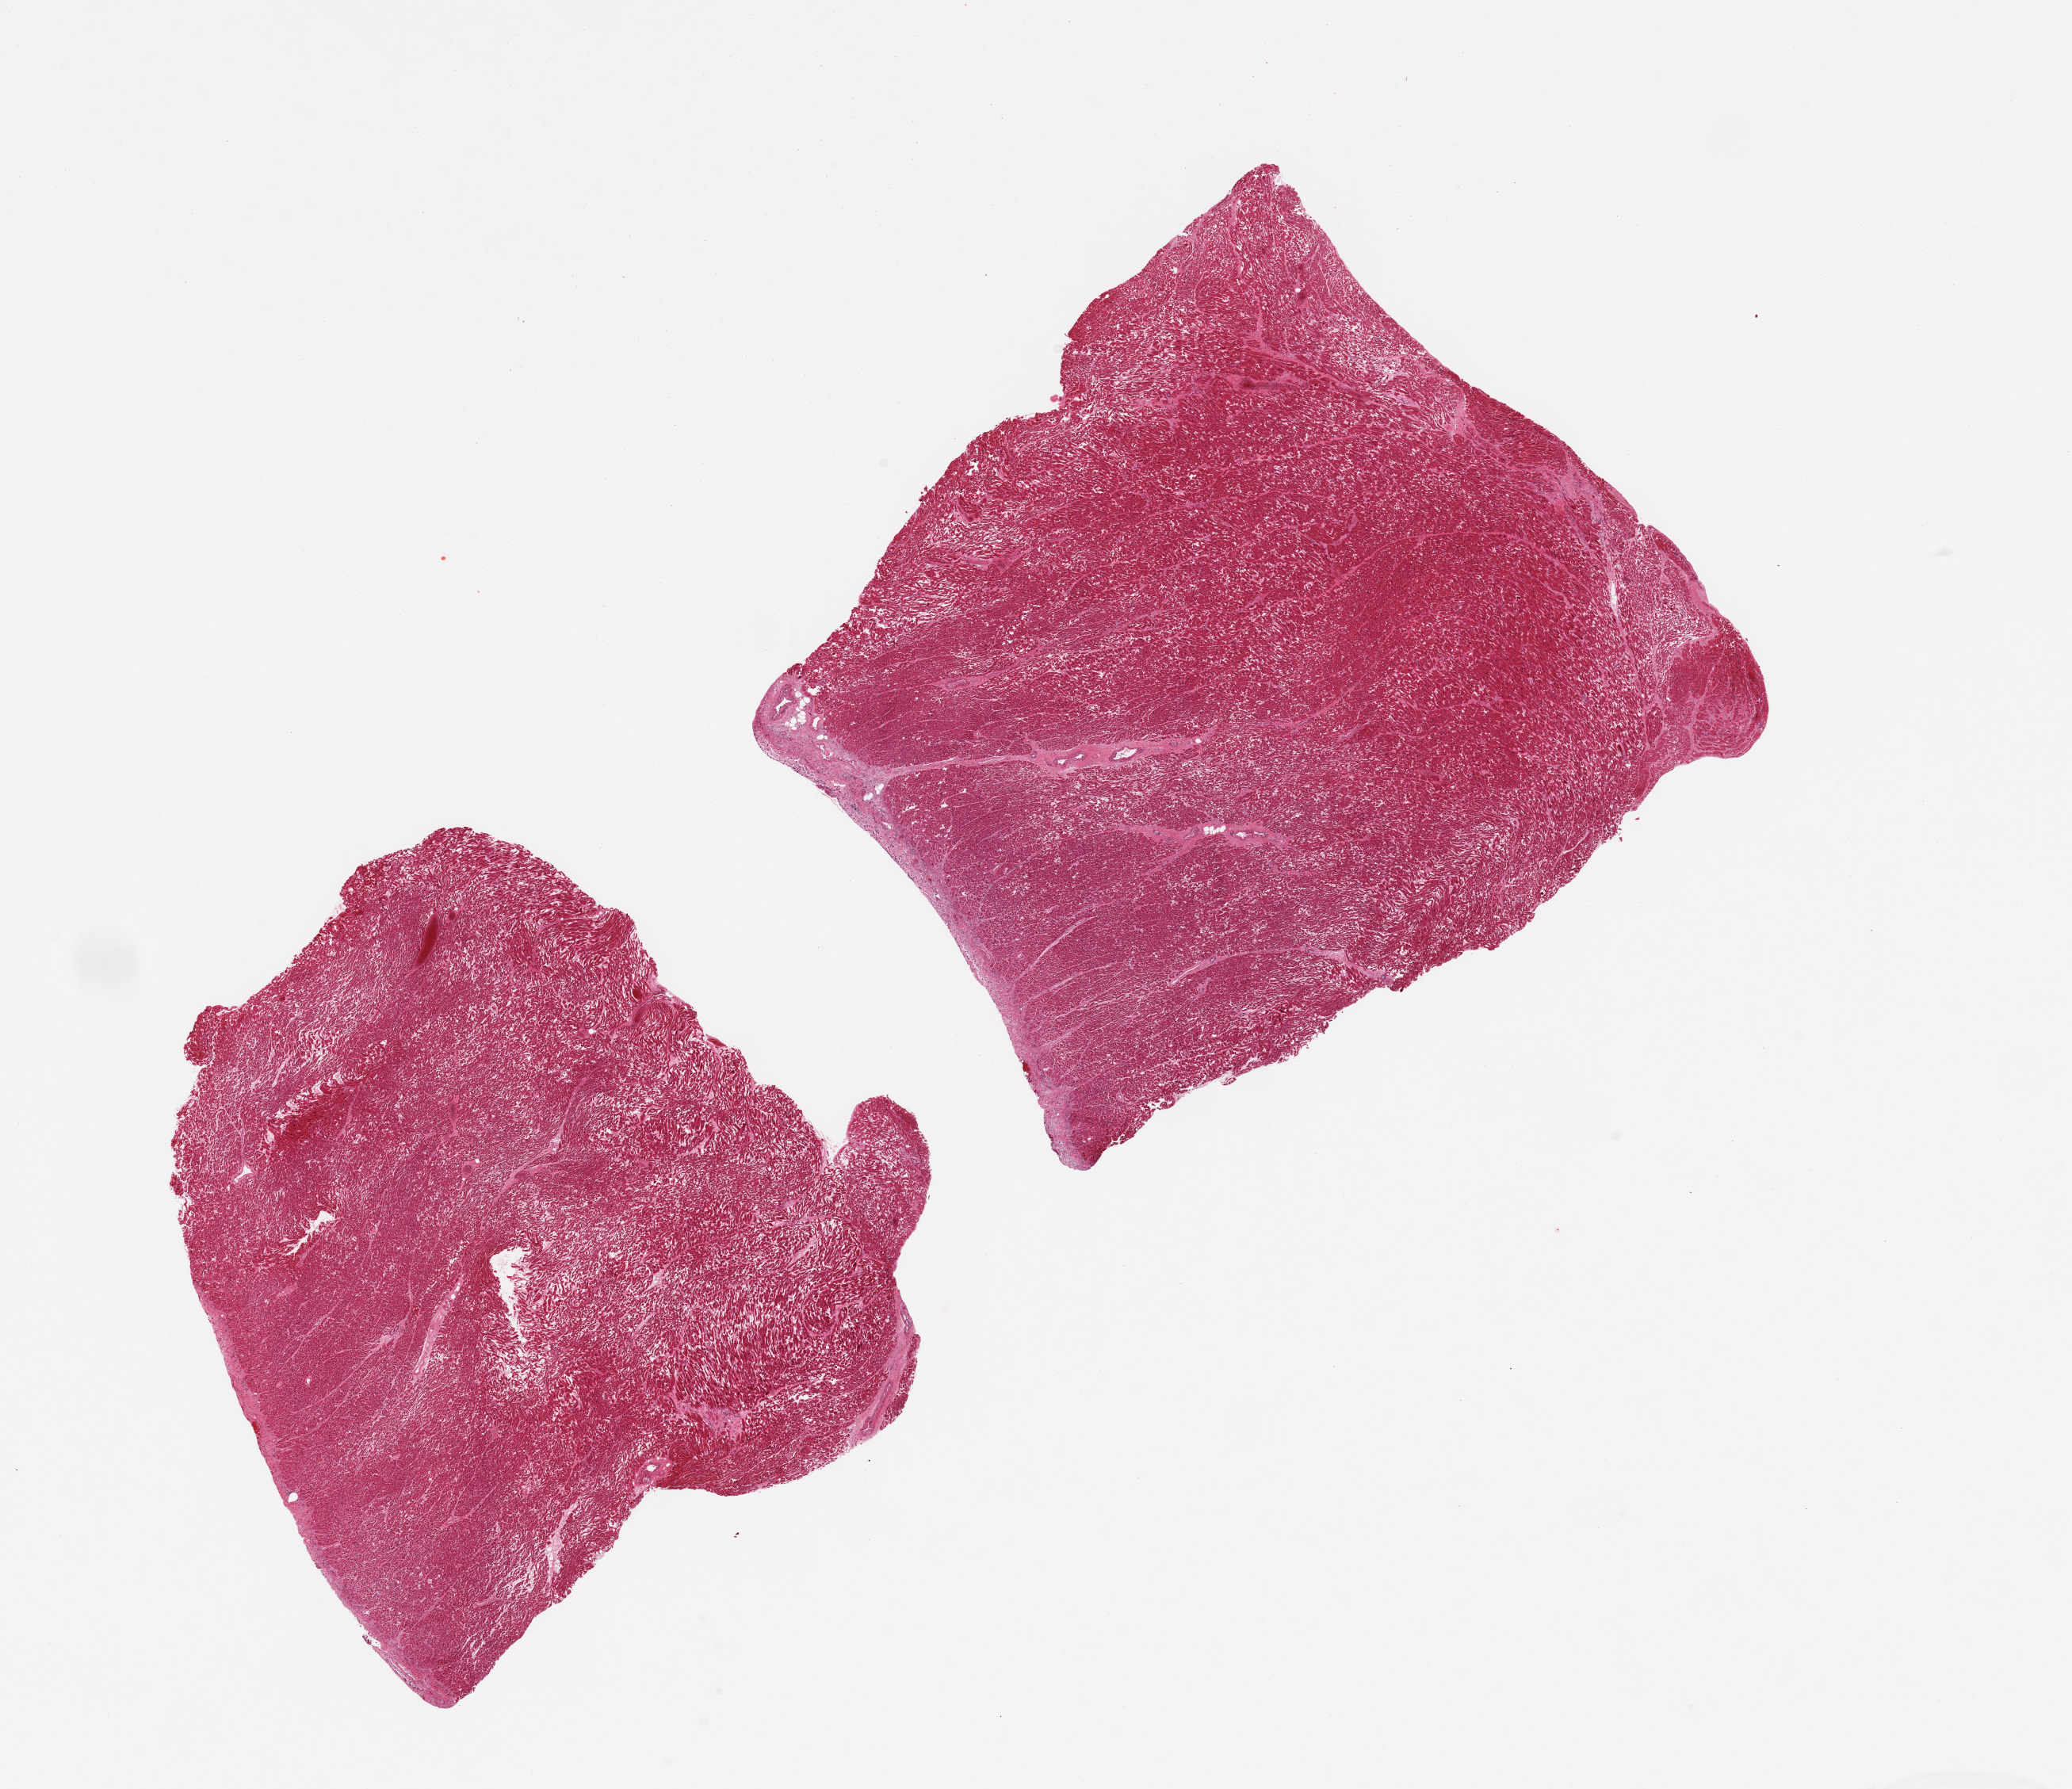
Digitized hematoxylin and eosin (H&E)-stained section — whole scanned area (about 20.7 x 17.8 mm, slide scanned at 20x) shown as a low-resolution overview; PAXgene-fixed, paraffin-embedded tissue; sampled site (target tissue): heart; donor tissue sample. Donor sex: male.
Review note (as recorded): 2 pieces, ~8x6mm unusually badly autolyzed.